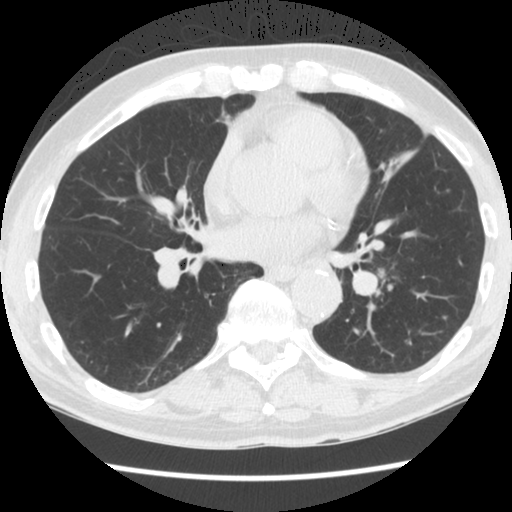
Low-dose screening chest CT, one axial slice. Slice 74 of 174 in the series (ordered by position). Reconstruction kernel STANDARD. 120 kVp. Lung window (W 1500 / L -600 HU). 512 × 512 image matrix, field of view 320 × 320 mm.
Outlined on this slice (manually delineated by an expert):
- lesion 1 (tumor, lower lobe of left lung): bounding box (x1, y1, x2, y2) in pixels: (376, 269, 388, 279)